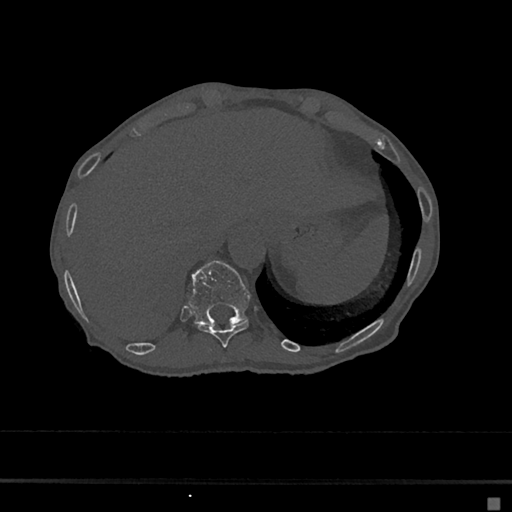
CT including the spine, one axial slice; position 200 of 797 along the scan axis; reconstruction kernel Br40s/3; 120 kVp; bone window (W 1800 / L 400 HU); 512 × 512 image matrix. Female patient, age 68 years. From the clinical record (not read from this slice): primary cancer: renal.
Structures marked on this image (semi-automatically segmented with operator editing):
- T10 vertebra: bounding box [x1, y1, x2, y2] px = [196, 320, 249, 347]
- T11 vertebra: [189, 261, 252, 324]